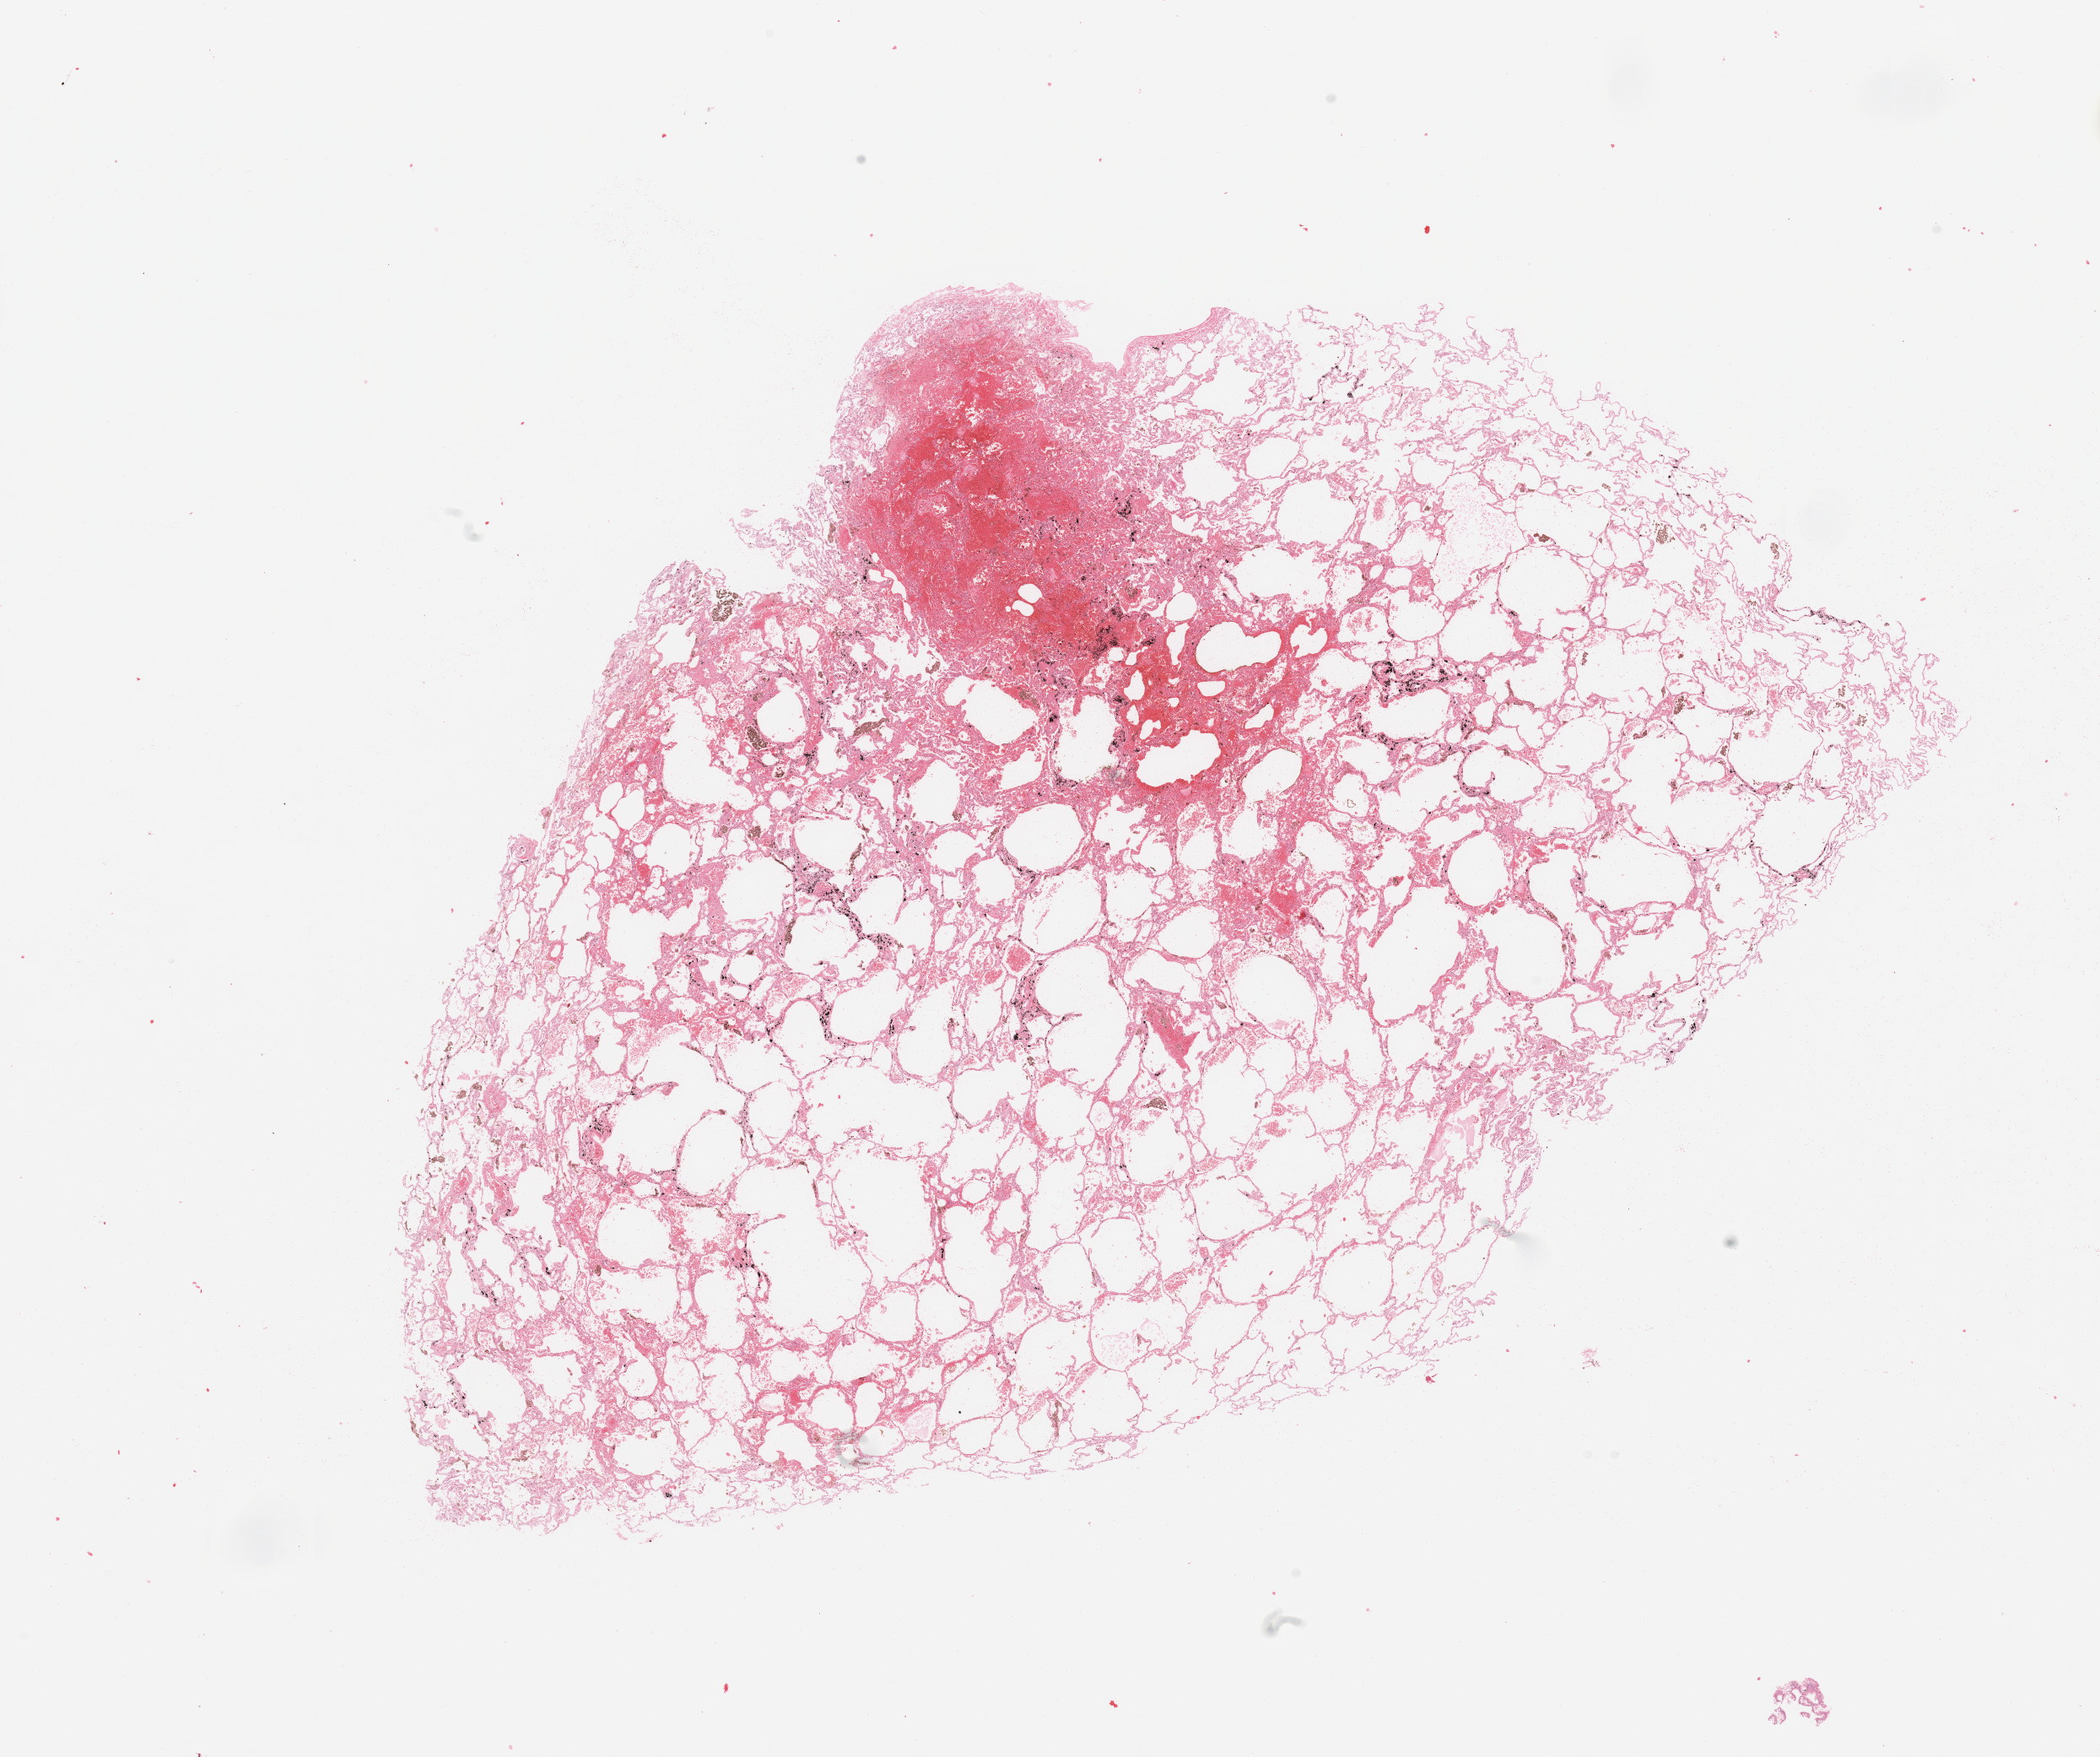
Whole-slide histology image, Hematoxylin and eosin (H&E) stained — a low-resolution overview of the entire scanned area, about 19.7 x 16.5 mm (acquisition: 20x scan), normal (non-tumour) tissue sample, lung. Patient: male, age 48 years.
* this section: normal (non-tumour) tissue from the same patient
* patient diagnosis: Adenocarcinoma, NOS